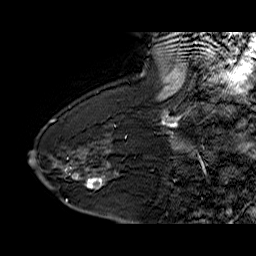
Breast MRI (dynamic contrast-enhanced), one sagittal slice. Dynamic contrast-enhanced series, time point 2 of 6 at this slice position (early post-contrast). 1.5 T. TE 6.4 ms, TR 32.9 ms. 256 × 256 image matrix. Female patient. From the clinical record (not read from this slice): setting: breast cancer imaged before/during neoadjuvant chemotherapy; receptor status: HR-positive, HER2-negative.
Structures marked on this image (semi-automatically segmented with operator editing):
- analysis volume of interest (the breast-tissue region the enhancement analysis was run in; not a lesion): bounding box <68,154,123,203> (left, top, right, bottom; pixels)
- tumour enhancement mask (voxels above the 100 % enhancement threshold inside the analysis volume of interest): <76,177,103,189>